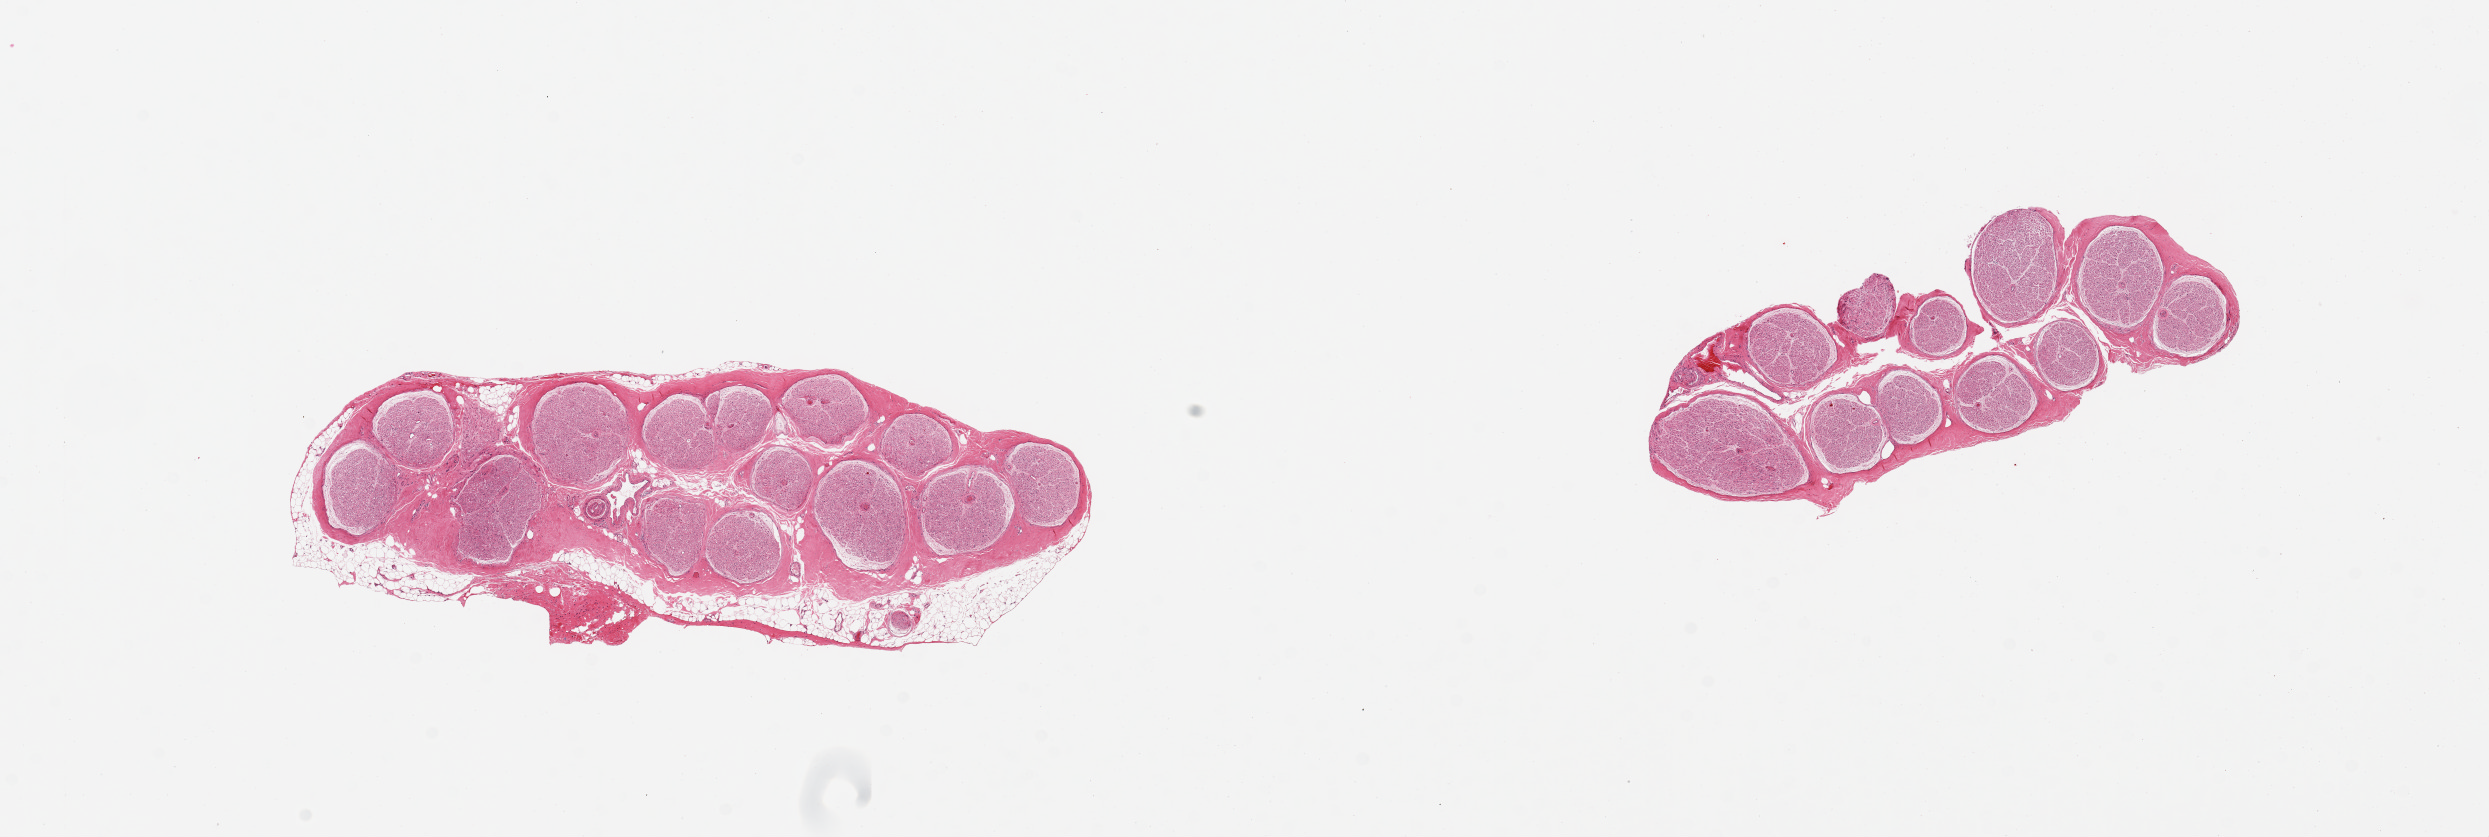
Whole-slide image, haematoxylin and eosin stain — shown as a low-resolution overview of the whole scanned area (about 19.7 x 6.6 mm, acquisition: 20x scan), PAXgene-fixed paraffin-embedded (PFPE) section, target tissue: tibial nerve, donor tissue sample.
• reviewer comment on this tissue sample: 2 pieces